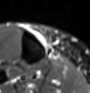
MRI of an extremity soft-tissue mass, one axial slice. Position 15 of 60 along the scan axis. STIR. MR volume resampled by the dataset authors to the PET/CT grid (not the native acquisition matrix). 3.27 mm slice thickness. 90 × 93 image matrix, field of view 88 × 91 mm. Female patient. Case-level facts recorded for this patient, not image findings: histological type: undifferentiated – high grade; grade: high; site of the primary tumour: right thigh.
Structures marked on this image (expert contour drawn on MRI and transferred to this co-registered scan by the dataset authors):
- gross tumour volume (mass): bounding box <37,33,52,50> (left, top, right, bottom; pixels)